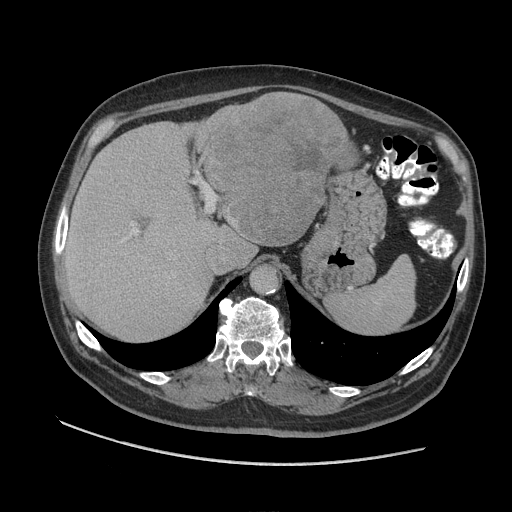
Contrast-enhanced abdominal CT (liver protocol), one axial slice. Slice 67 of 109 in the series (ordered by position). Reconstruction kernel STANDARD. Soft-tissue window (W 400 / L 40 HU). 2.5 mm slice thickness. 512 × 512 image matrix, field of view 420 × 420 mm. Case-level facts recorded for this patient, not image findings: diagnosis: hepatocellular carcinoma (patient treated with transarterial chemoembolisation; whether this scan precedes or follows treatment is not stated here); TNM stage (as recorded): Stage-I; Child-Pugh class: A.
Structures marked on this image (semi-automatic segmentation, software-assisted and operator-edited):
- liver parenchyma outside the tumour (the mass and vessels are separate outlines, so this box may not span the whole liver): bounding box <64,116,278,340> (left, top, right, bottom; pixels)
- mass: <188,91,360,244>
- liver vessels: <122,223,137,242>